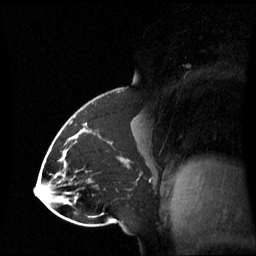
Breast MRI (dynamic contrast-enhanced), one sagittal slice. Position 33 of 60 along the scan axis. Dynamic contrast-enhanced series, image 2 of 3 at this slice position (ordered by acquisition). 1.5 T. TE 4.2 ms, TR 8.4 ms. 2.8 mm slice thickness. 256 × 256 image matrix. Patient: female, 43 years. From the clinical record (not read from this slice): setting: breast cancer imaged before/during neoadjuvant chemotherapy; receptor status: triple-negative.
Structures marked on this image (semi-automatic segmentation, software-assisted and operator-edited):
- analysis volume of interest (the breast-tissue region the enhancement analysis was run in; not a lesion): box from (x=65, y=118) to (x=143, y=198) px
- tumour enhancement mask (voxels above the 70 % enhancement threshold inside the analysis volume of interest): (x=67, y=138)–(x=129, y=163)